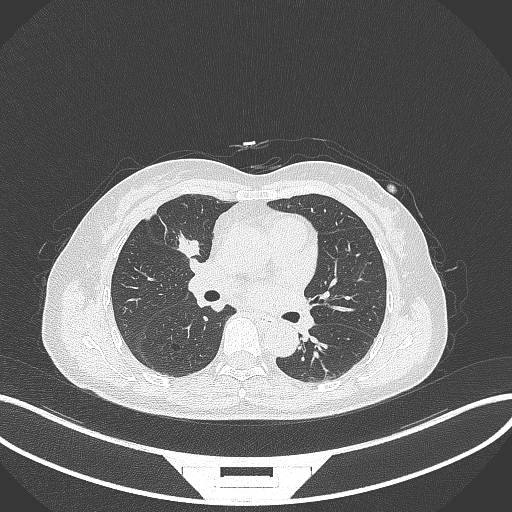
Chest CT, one axial slice. 120 kVp. Lung window (W 1500 / L -600 HU). 1 mm slice thickness. 512 × 512 image matrix, field of view 400 × 400 mm. Patient: female, 51 years. From the clinical record (not read from this slice): clinical TNM (as recorded): T1c N0 M0; histopathological grade: G2.
Structures marked on this image (rectangle marked by the reading radiologist):
- lung tumour (recorded histology: adenocarcinoma): bounding box (x1, y1, x2, y2) in pixels: (175, 229, 204, 263)